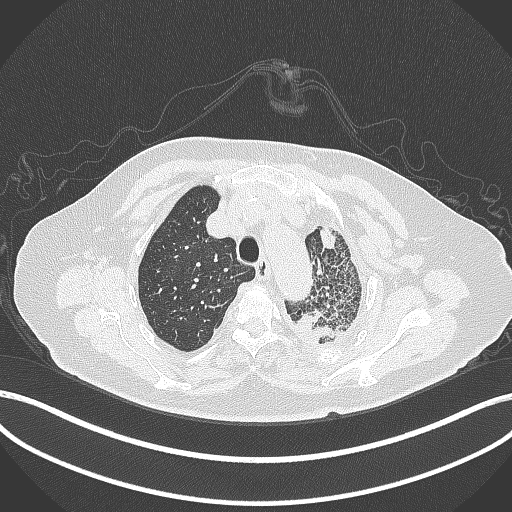
Chest CT, one axial slice. Position 316 of 399 along the scan axis. 120 kVp. Lung window (W 1500 / L -600 HU). 512 × 512 image matrix. Patient: female, 75 years. From the clinical record (not read from this slice): clinical TNM (as recorded): T3 N3 M1.
Outlined on this slice (rectangle marked by the reading radiologist):
- lung tumour (recorded histology: adenocarcinoma): bounding box (x1, y1, x2, y2) in pixels: (291, 303, 348, 351)